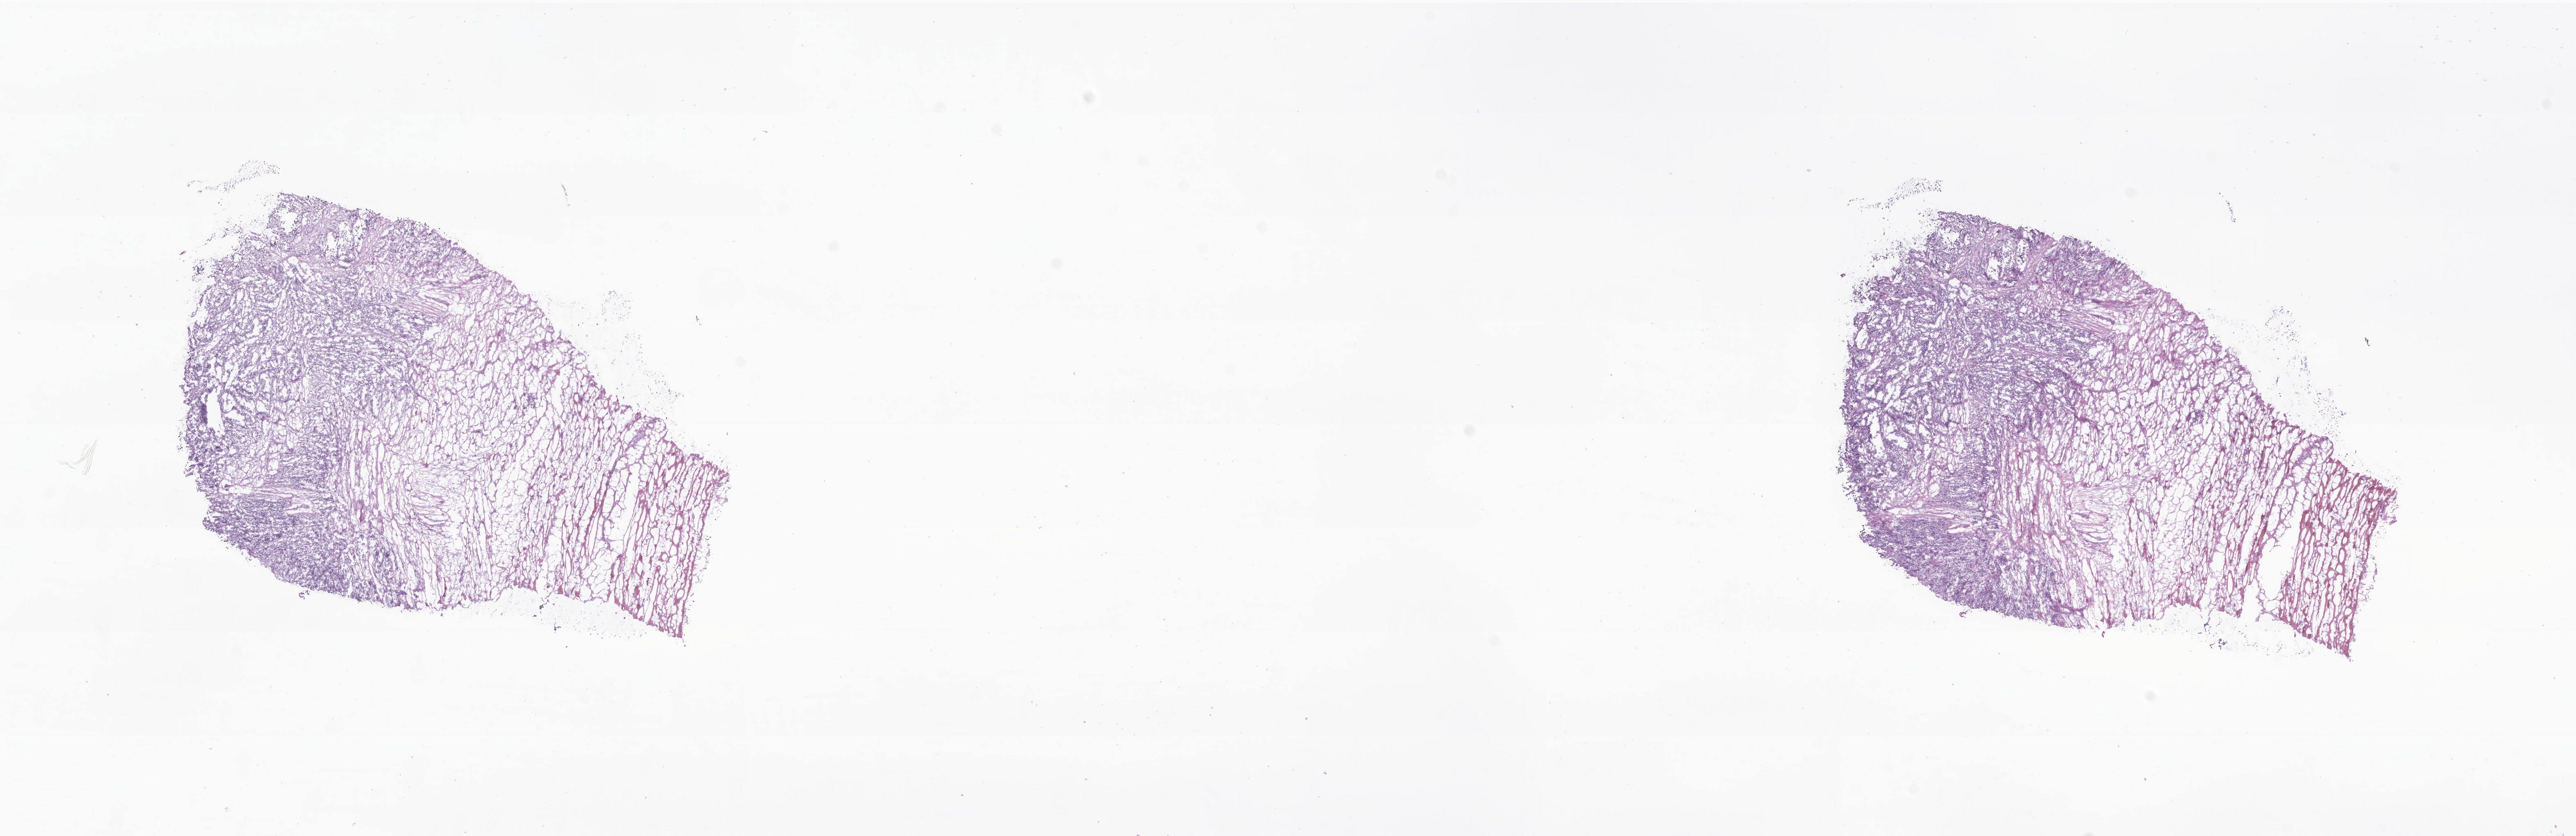
Whole-slide image, haematoxylin and eosin stain of tumor tissue from the lower limb, whole scanned area (about 26.5 x 8.6 mm) shown as a low-resolution overview; frozen section (OCT-embedded). Male patient, age 235 months (19 years 7 months).
Recorded diagnosis: Alveolar rhabdomyosarcoma.